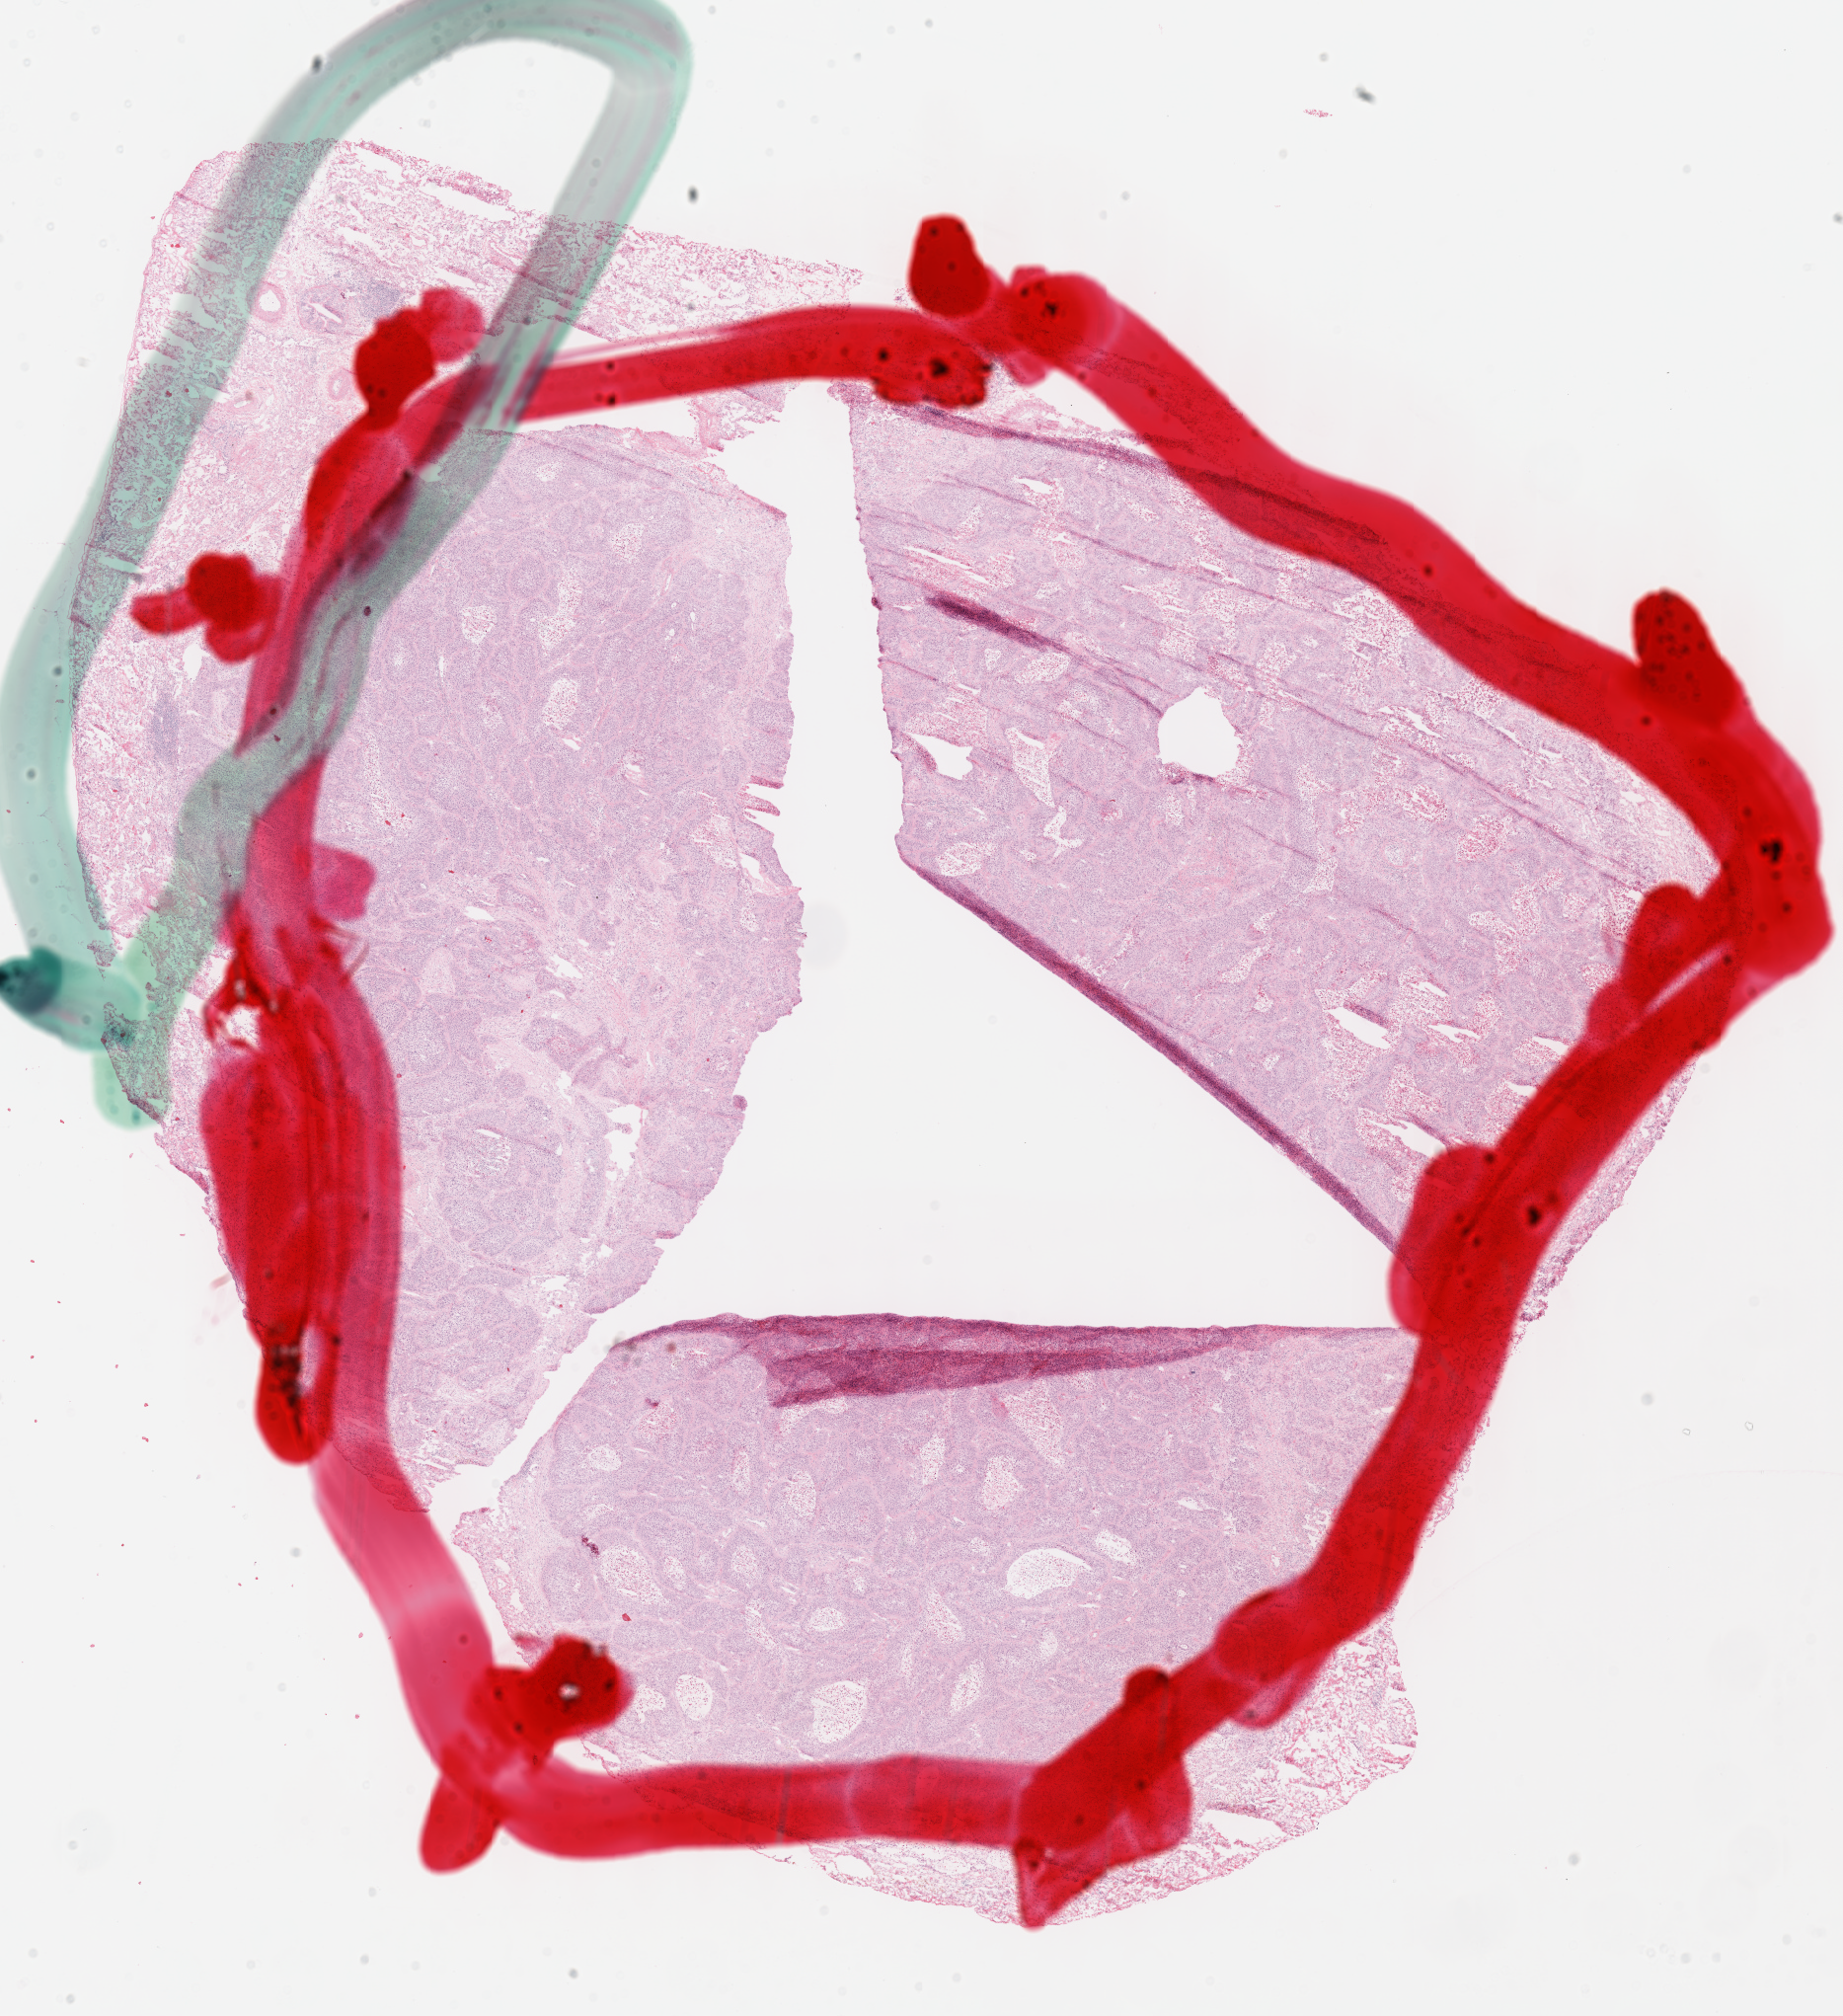
Digitized Hematoxylin and eosin (H&E) stained tissue section (whole slide) — a low-resolution overview of the entire scanned area, about 14.7 x 16.1 mm; frozen section from the top of the tissue portion; primary tumour sample from the lung. Female patient; age at initial diagnosis 59 years. Pathologist review of this section (percent, as recorded): tumour cells 95%, tumour nuclei 80%, normal cells 0%, stromal cells 0%, necrosis 5%. Infiltration values recorded for this section: lymphocyte infiltration 2%, monocyte infiltration 5%, neutrophil infiltration 0%.
AJCC pathologic stage: IA. Pathologic diagnosis: Squamous cell carcinoma, NOS (upper lobe, lung). Laterality: left.